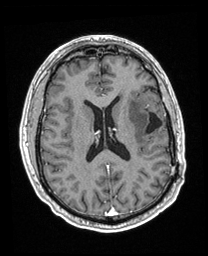
Brain MRI from a brain-tumour surgery series, one axial slice; slice 94 of 208 in the series (ordered by position); T1-weighted post-contrast; 1 mm slice thickness; 208 × 256 image matrix. Case-level facts recorded for this patient, not image findings: histopathology: Astrocytoma; WHO grade: 3; IDH mutation: yes; tumour location: Left Insular.
Structures marked on this image (expert manual segmentation):
- previous resection cavity: bounding box [x1, y1, x2, y2] px = [146, 113, 163, 134]